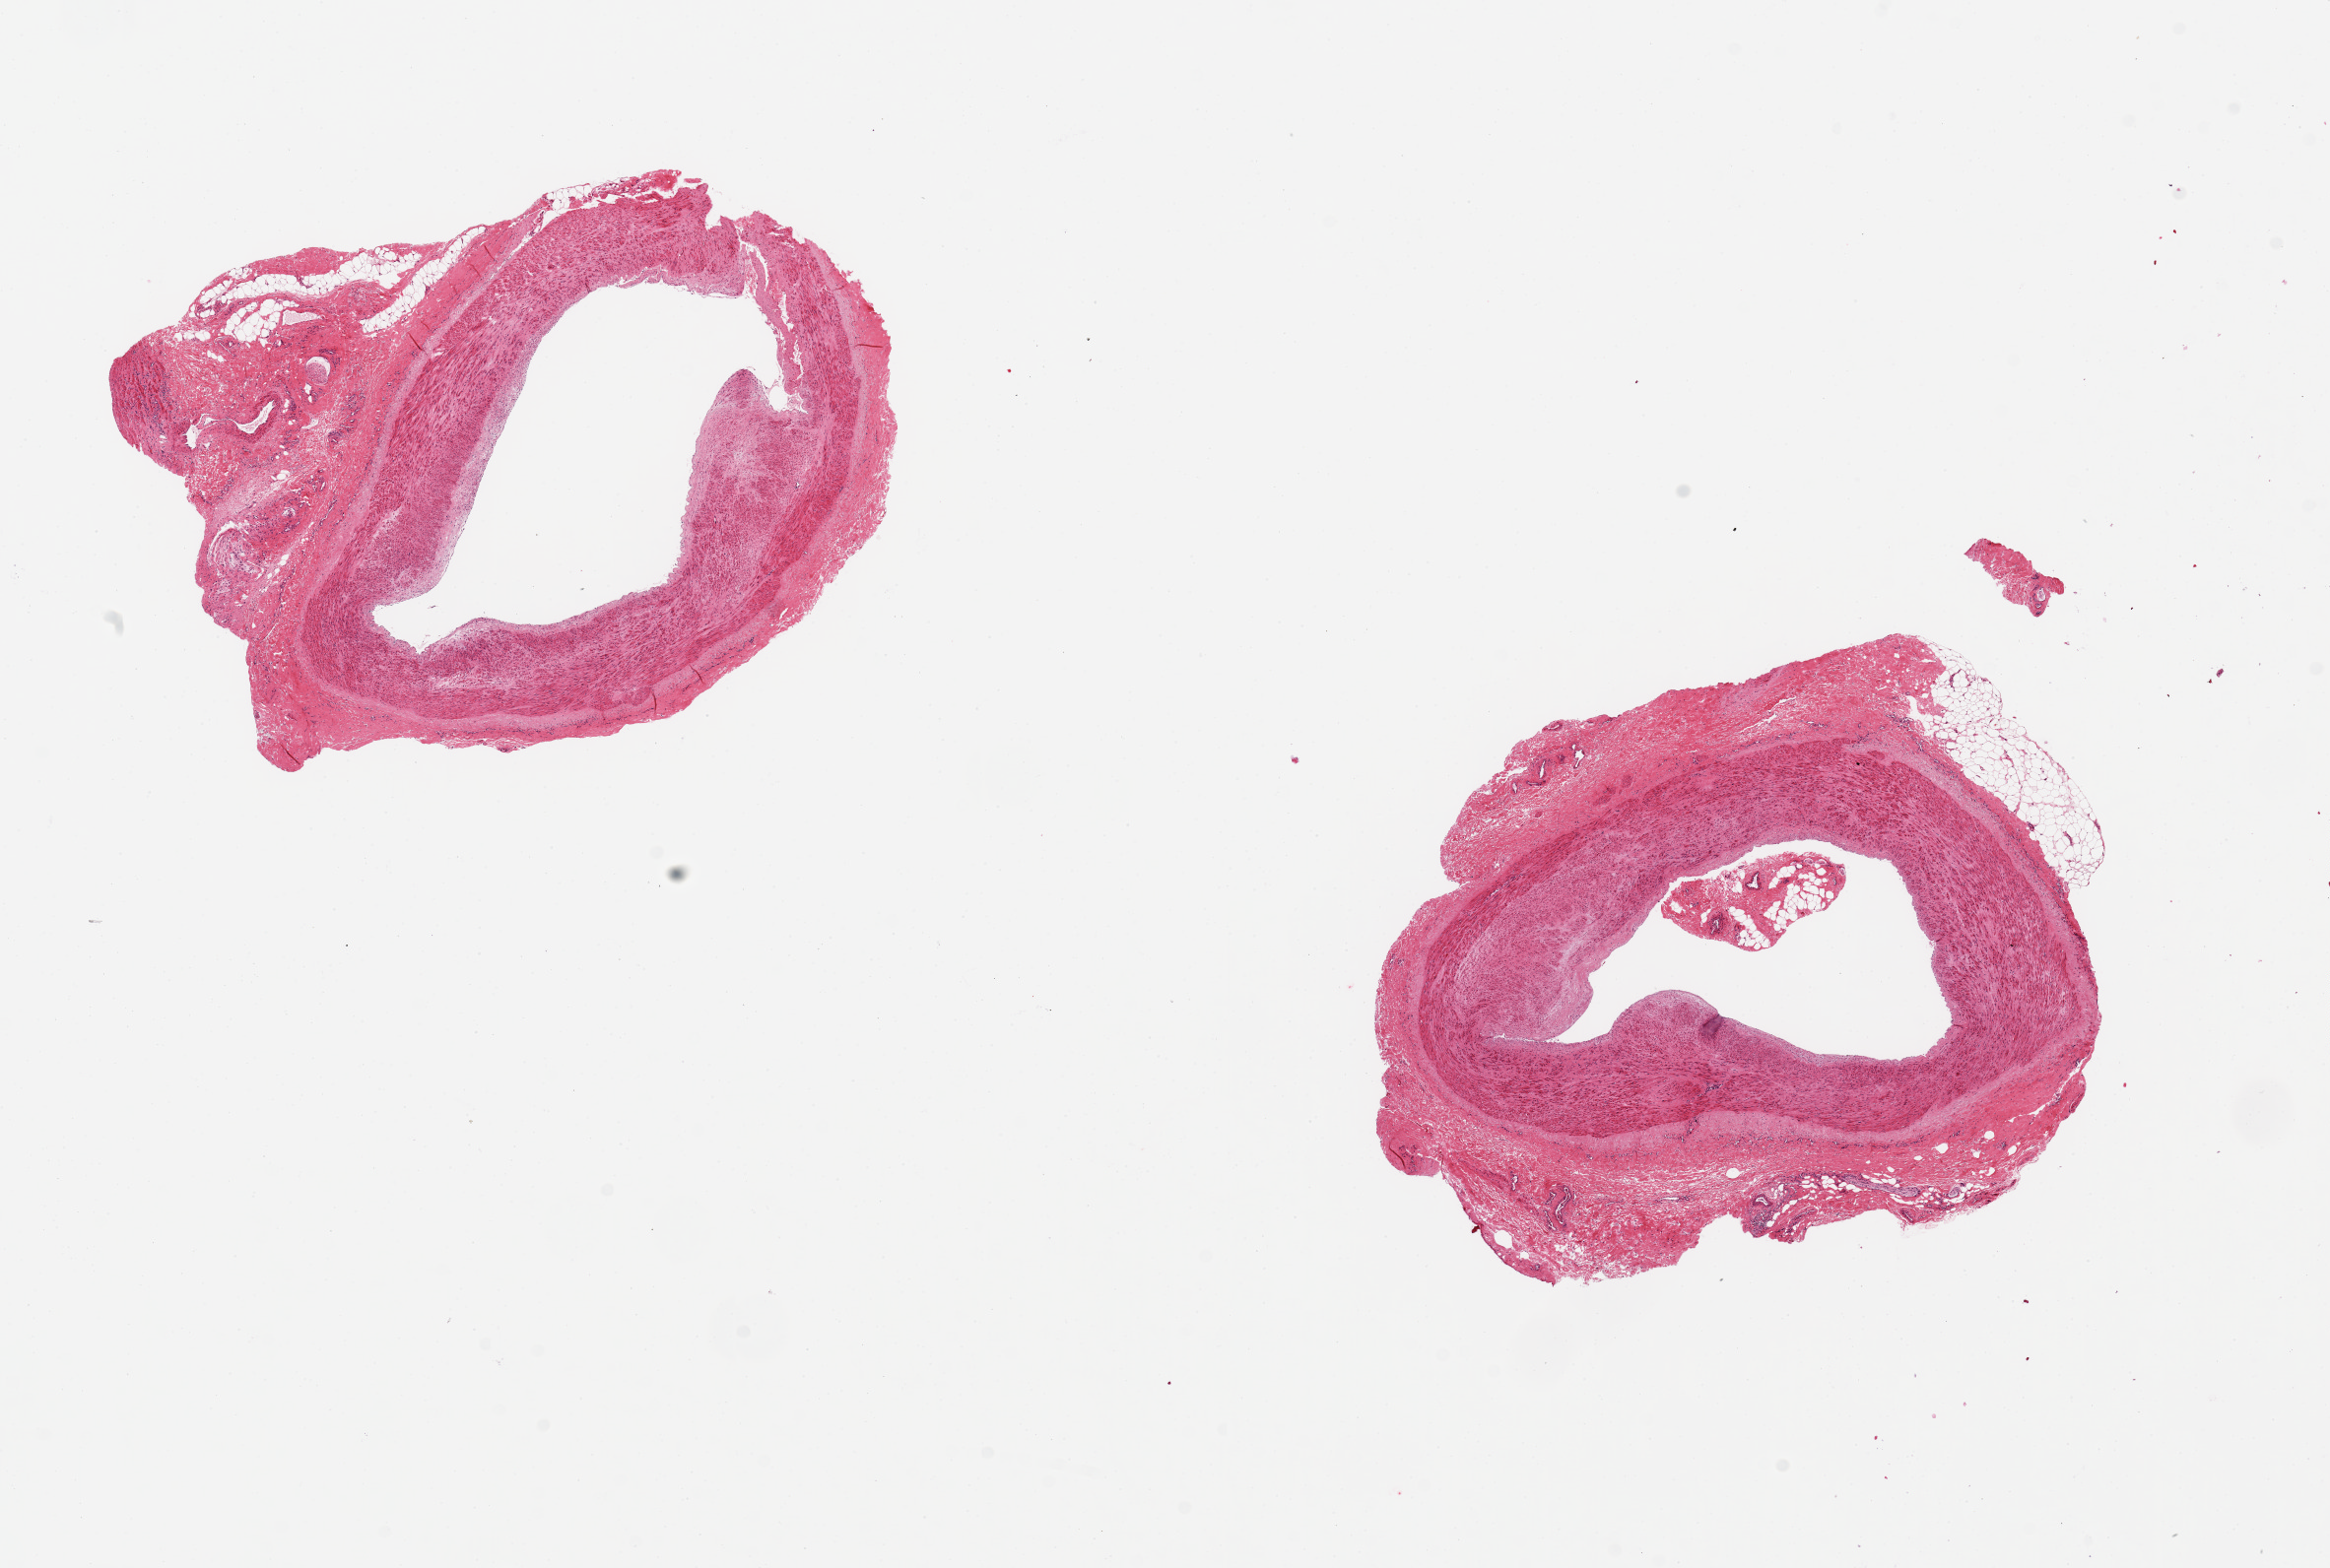
Whole-slide image, hematoxylin and eosin (H&E) stain — a low-resolution overview of the entire scanned area, about 18.7 x 12.6 mm (slide scanned at 20x); PAXgene-fixed paraffin-embedded (PFPE) section; sampled site (target tissue): tibial artery; tissue donor sample. Donor sex: male.
Reviewer comment on this tissue sample: 2 pieces ~5mm d; Adherent fibroadipose tissue, discontinuous, up to ~2mm.